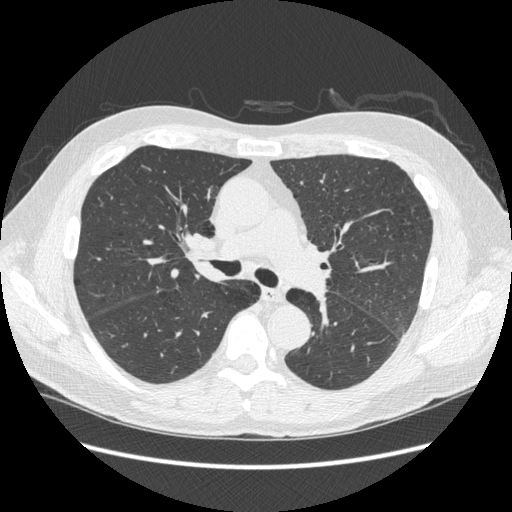
Axial slice from a low-dose chest CT screening exam. Third screening round (two years after baseline). Lung window (W 1500 / L -600 HU). 1.25 mm slice thickness. Standard (soft-tissue) reconstruction kernel (STANDARD). 120 kVp. Slice 106 of 258 in the series. 512 × 512 image matrix. Male, age 59 years at enrolment.
• Expert-annotated lung lesion, bounding box <179,225,229,268> (left, top, right, bottom; pixels).
• The screening reader recorded 2 non-calcified nodules or masses ≥4 mm on this exam (right upper lobe, left lower lobe); which of them this box marks is not recorded.
• Official screen result: negative screen, minor abnormalities not suspicious for lung cancer.
• Later outcome: lung cancer diagnosed 169 days after this screen — squamous cell carcinoma, keratinizing, NOS, right hilum, stage IIIB (AJCC 6th edition).